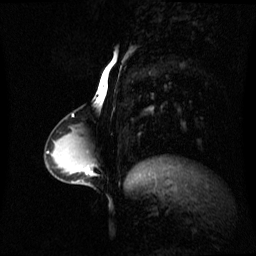
Breast MRI (dynamic contrast-enhanced), one sagittal slice; position 25 of 60 along the scan axis; dynamic contrast-enhanced series, image 2 of 3 at this slice position (ordered by acquisition); 1.5 T; TE 4.2 ms, TR 8.4 ms; 256 × 256 image matrix. Female patient, age 34 years. From the clinical record (not read from this slice): setting: breast cancer imaged before/during neoadjuvant chemotherapy; receptor status: triple-negative.
Structures marked on this image (semi-automatic segmentation, software-assisted and operator-edited):
- analysis volume of interest (the breast-tissue region the enhancement analysis was run in; not a lesion): bounding box <57,156,91,185> (left, top, right, bottom; pixels)
- tumour enhancement mask (voxels above the 70 % enhancement threshold inside the analysis volume of interest): <85,168,91,173>